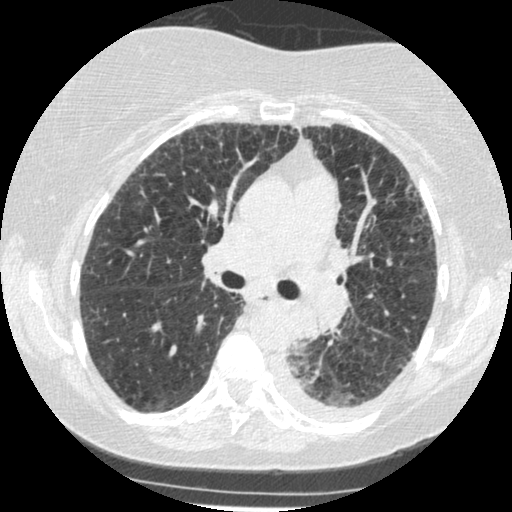
Low-dose screening chest CT, axial slice; third screening round (two years after baseline); lung window (W 1500 / L -600 HU); 1.25 mm slice thickness; standard (soft-tissue) reconstruction kernel (STANDARD); 120 kVp; slice 182 of 341 in the series. Female, age 60 years at enrolment. Former smoker at enrolment.
• Lesion marked by an expert reader, bounding box (x1, y1, x2, y2) in pixels: (268, 308, 341, 373).
• The exam's reader record, not a measurement of the box and not confirmed to be the same lesion: non-calcified nodule or mass ≥4 mm, left lower lobe, 54 × 38 mm, smooth margins, soft tissue attenuation, pre-existing on the prior screen: yes; interval growth: yes.
• Official screen result: positive, other.
• Later outcome: lung cancer diagnosed 15 days after this screen — small cell carcinoma, NOS, left lower lobe, undifferentiated (G4), stage IV (AJCC 6th edition), 69 mm at pathology.